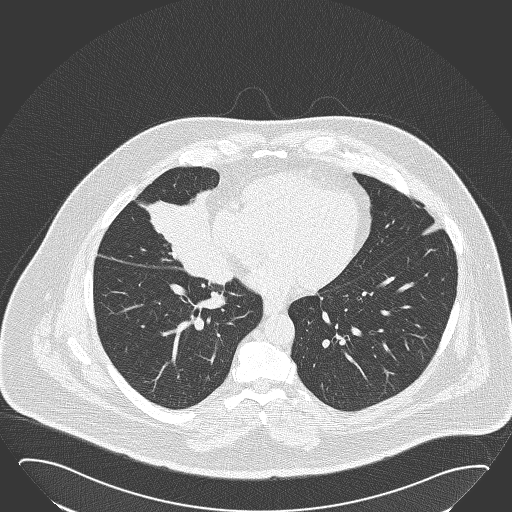
Axial slice from a low-dose chest CT screening exam, baseline annual screen, lung window (W 1500 / L -600 HU), 2 mm slice thickness, 120 kVp. Male participant, aged 61 years at enrolment. Former smoker at enrolment.
Expert-annotated lung lesion, bounding box (x1, y1, x2, y2) in pixels: (137, 180, 228, 269). The screening reader recorded 2 non-calcified nodules or masses ≥4 mm on this exam (right middle lobe, left lower lobe); which of them this box marks is not recorded. Later outcome: lung cancer diagnosed 47 days after this screen — basaloid squamous cell carcinoma, right middle lobe, right hilum, poorly differentiated (G3), stage IIB (AJCC 6th edition), 95 mm at pathology.